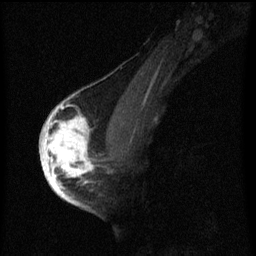
Breast MRI (dynamic contrast-enhanced), one sagittal slice. Slice 38 of 60 in the series (ordered by position). Dynamic contrast-enhanced series, image 2 of 3 at this slice position (ordered by acquisition). 1.5 T. TE 4.2 ms, TR 8 ms. 2 mm slice thickness. 256 × 256 image matrix, field of view 180 × 180 mm. Female patient, age 56 years.
Outlined on this slice (semi-automatic segmentation, software-assisted and operator-edited):
- analysis volume of interest (the breast-tissue region the enhancement analysis was run in; not a lesion): bounding box [x1, y1, x2, y2] px = [42, 110, 97, 193]
- tumour enhancement mask (voxels above the 70 % enhancement threshold inside the analysis volume of interest): [42, 110, 95, 193]